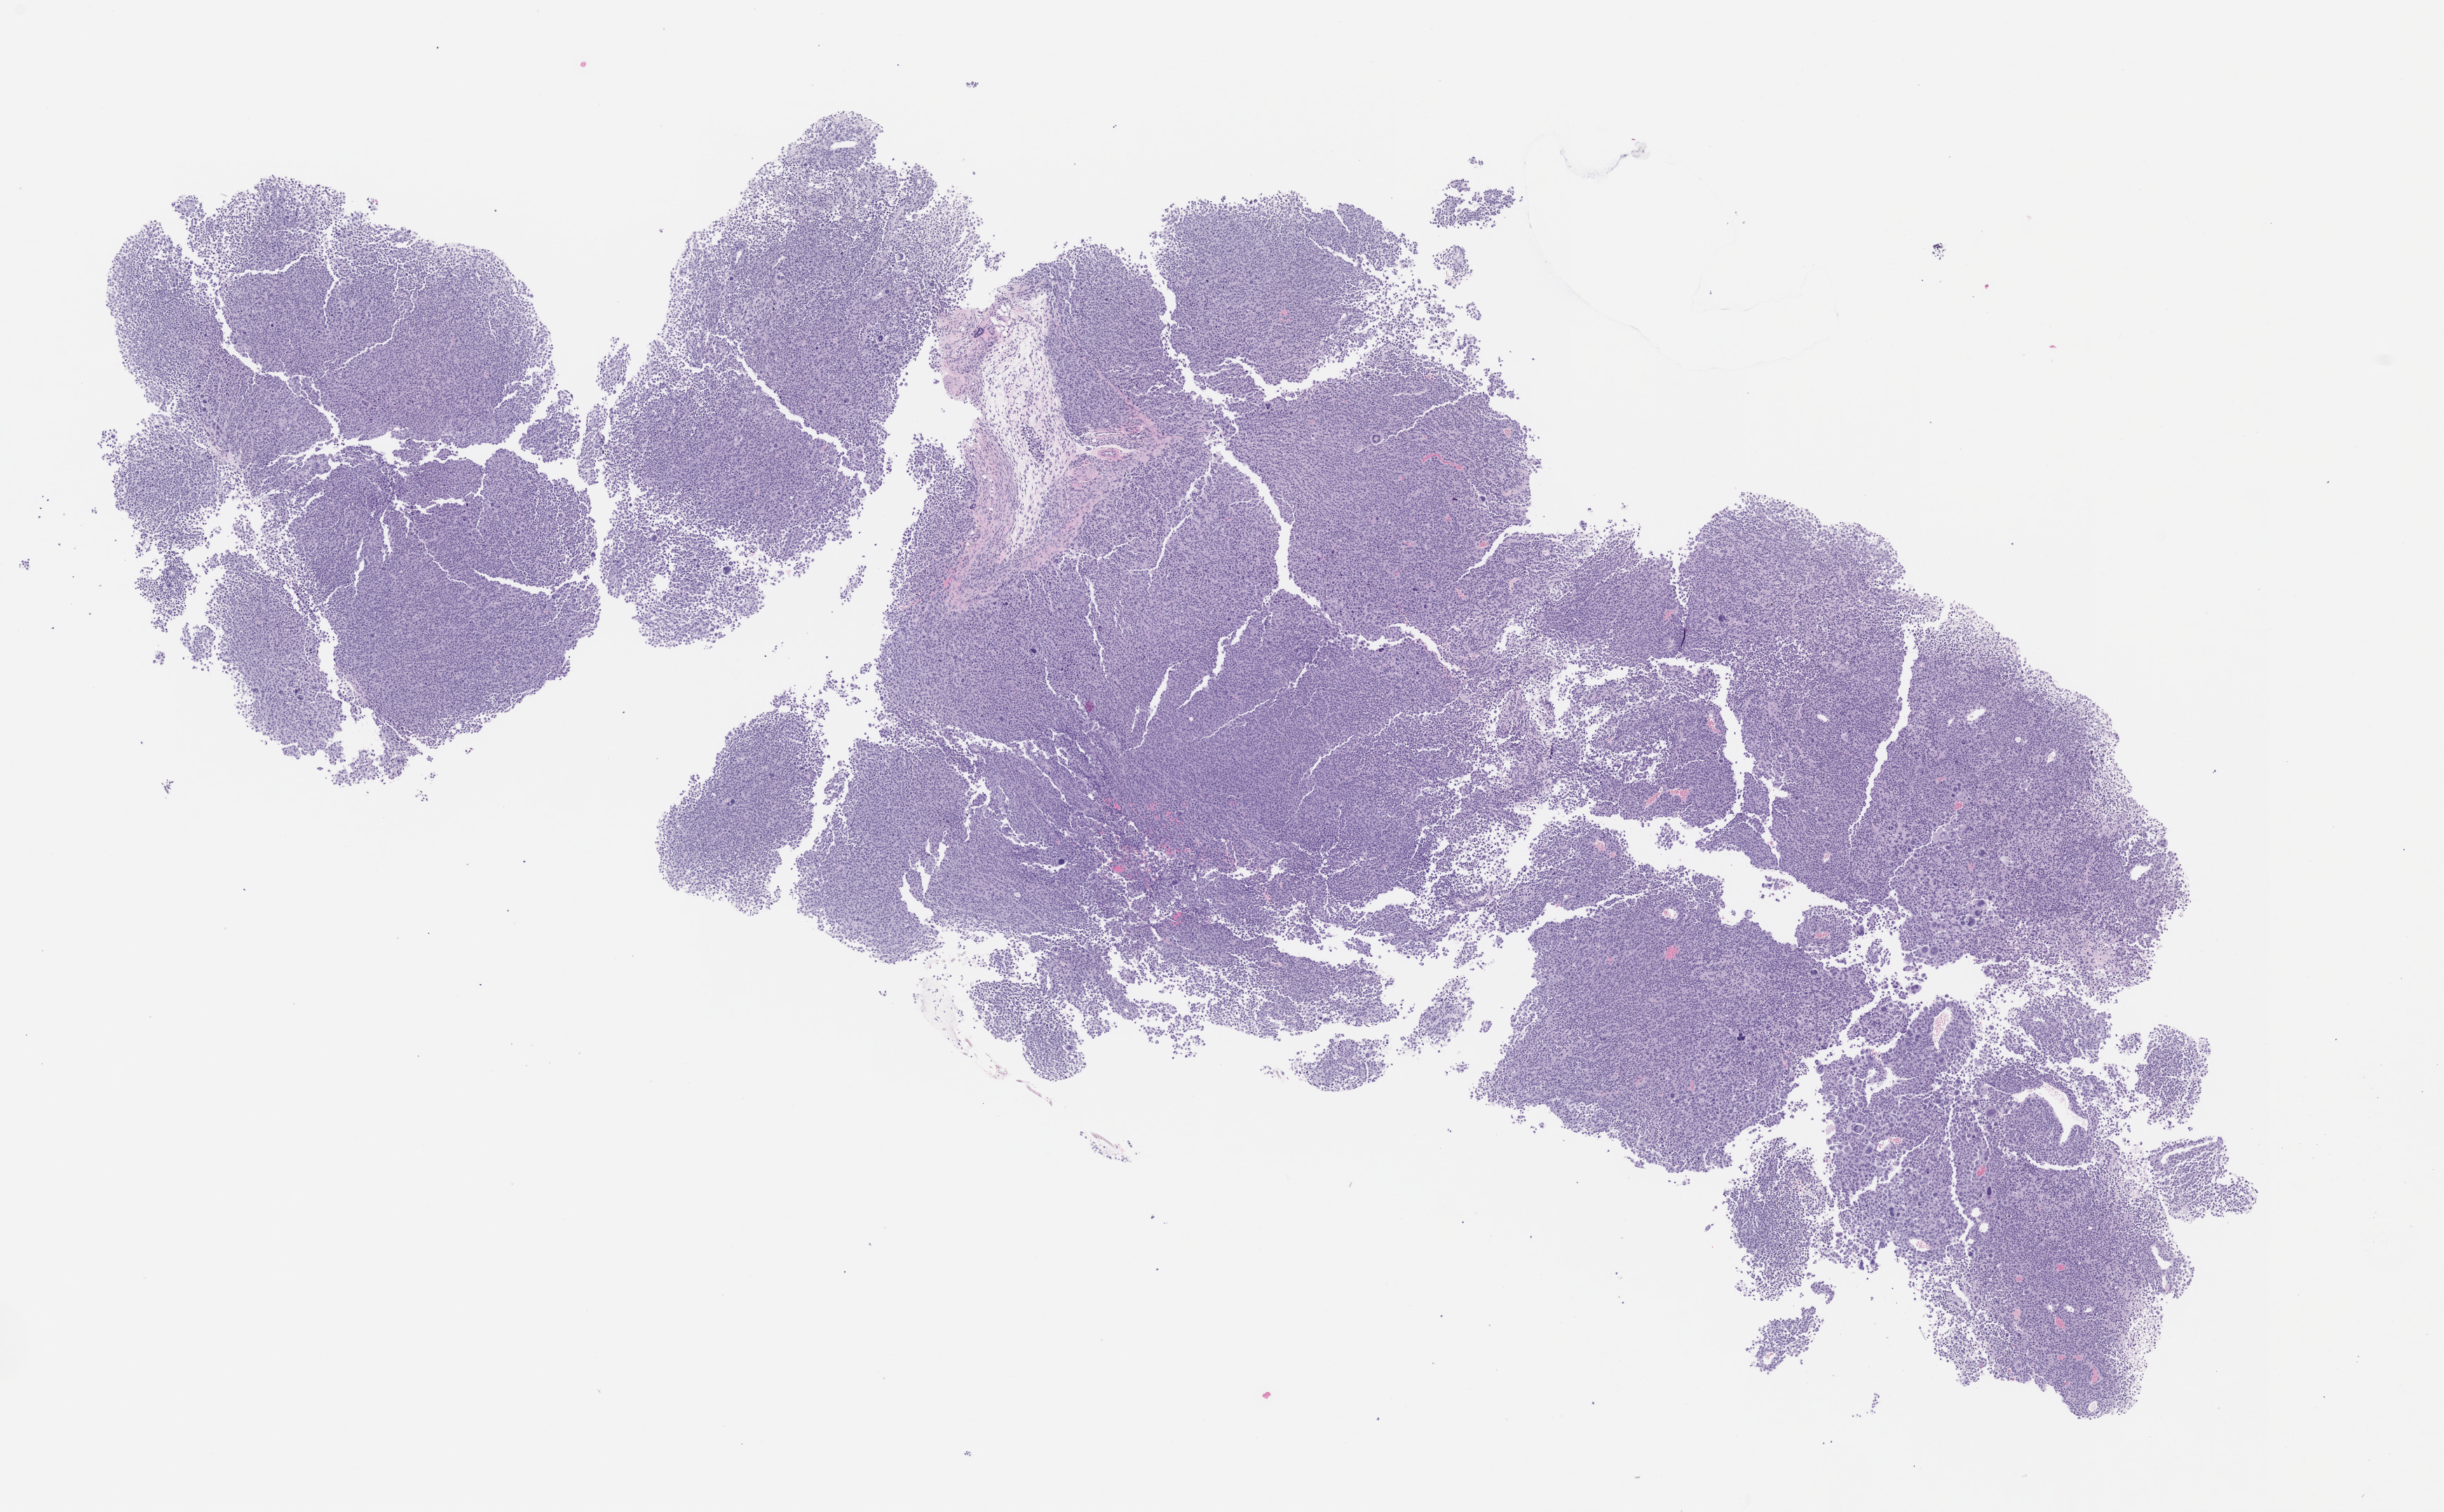
Hematoxylin and eosin (H&E) whole-slide image of a patient-derived xenograft (PDX) tumor grown in a mouse, passage 0, a low-resolution overview of the entire scanned area, about 14.0 x 8.7 mm, FFPE section, originating tumor site category: skin.
Originating patient diagnosis: Melanoma.